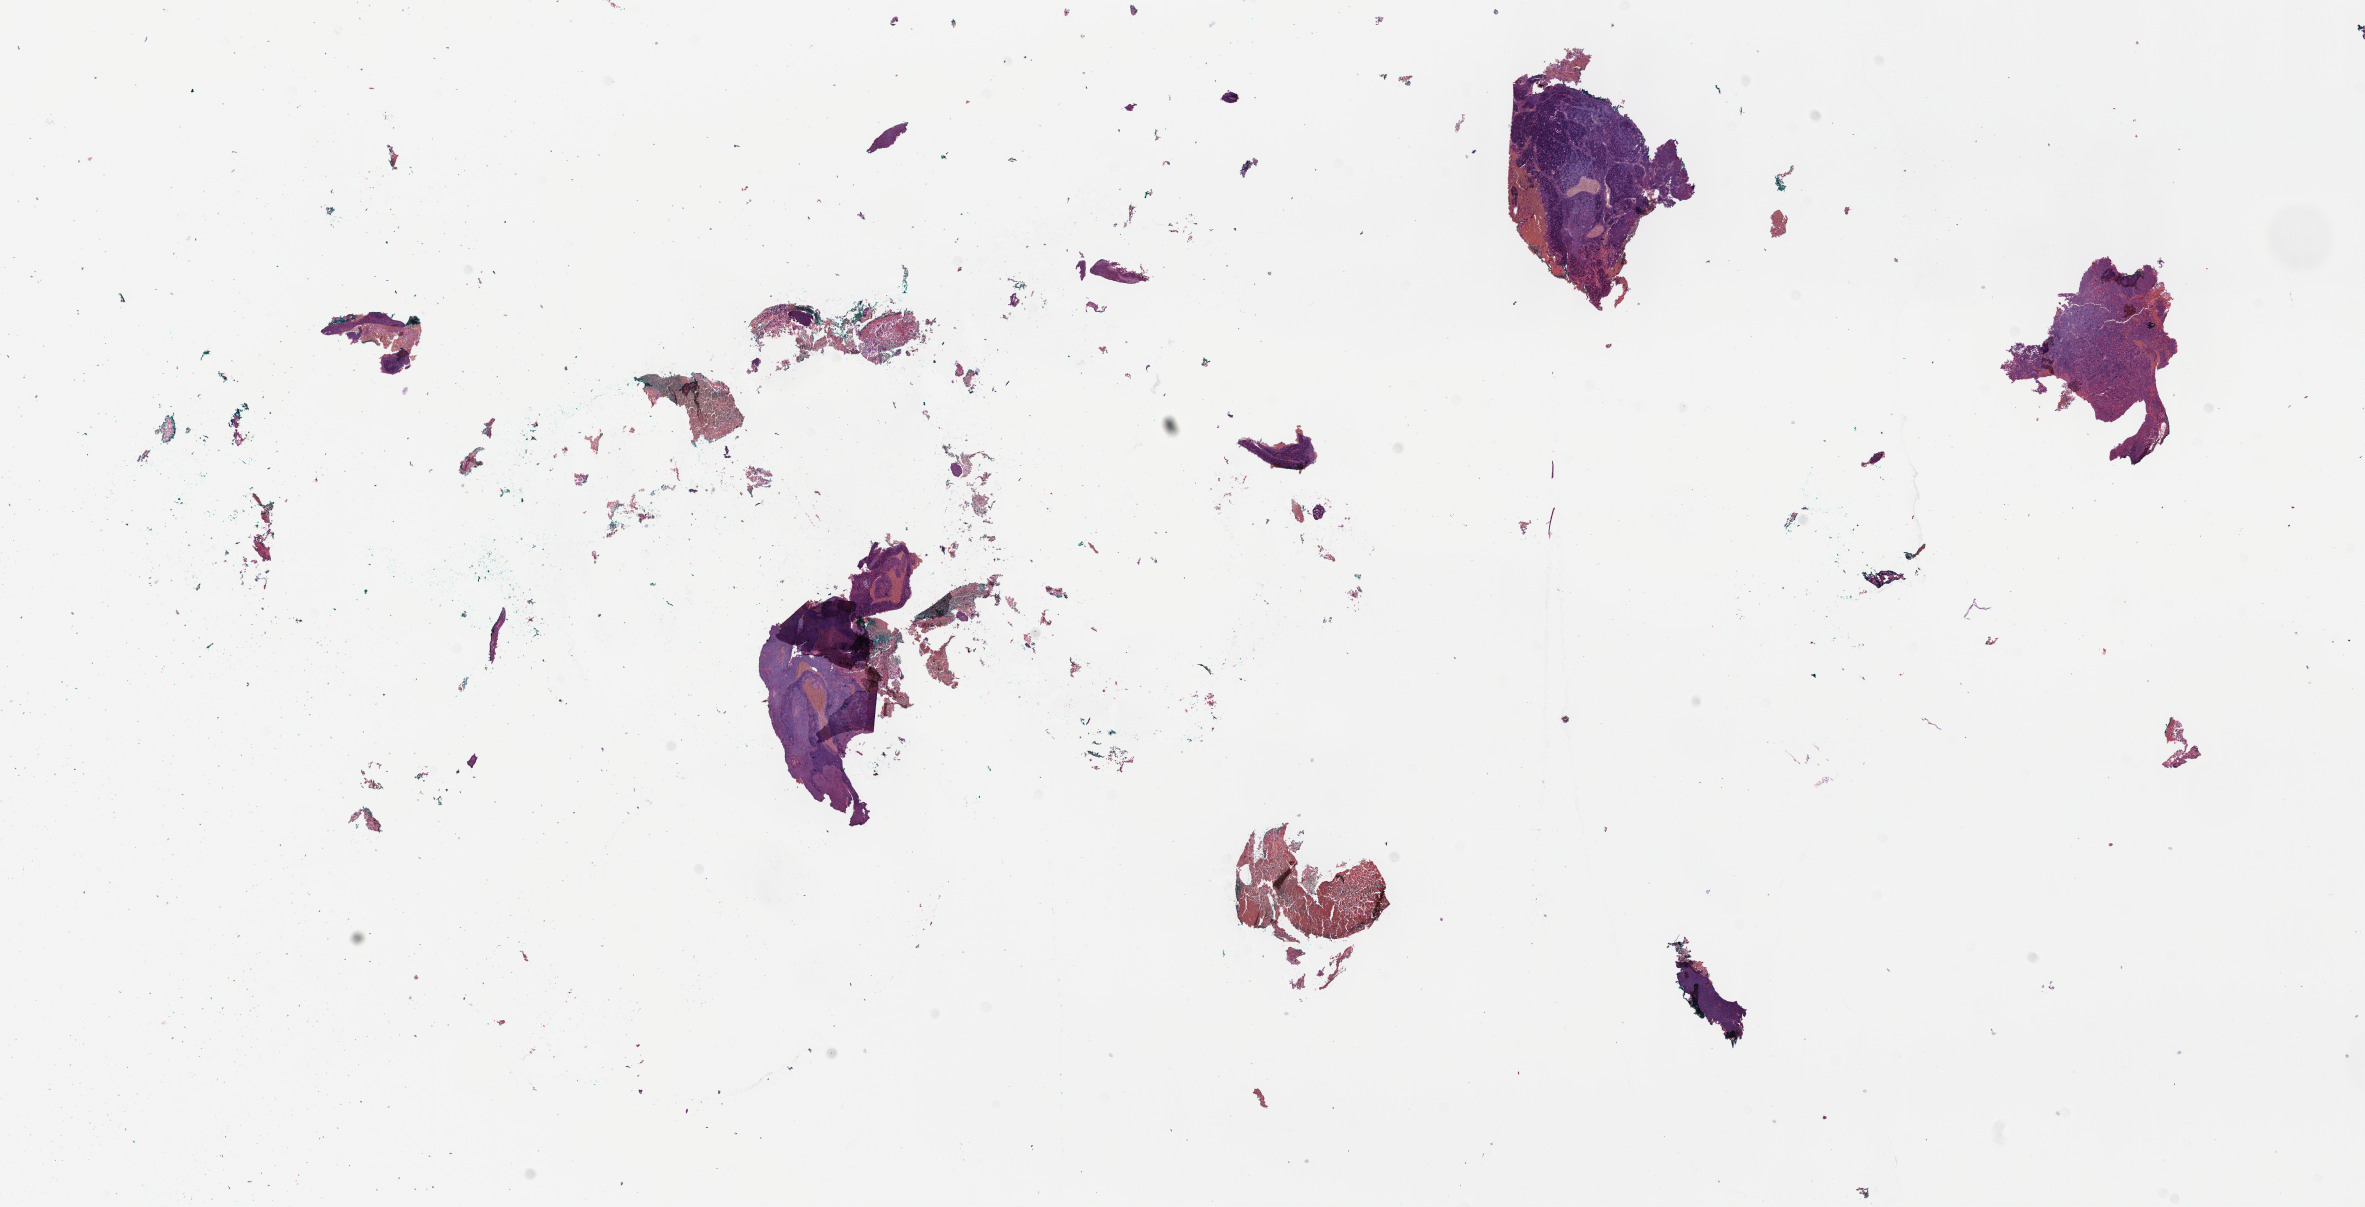
Whole-slide histology image, Hematoxylin and eosin (H&E) stained, shown as a low-resolution overview of the whole scanned area (about 19.1 x 9.8 mm), formalin-fixed paraffin-embedded (FFPE) diagnostic section, cervix, primary tumour sample. Patient: female, age at initial diagnosis 62 years. Histologic grade: G3 (poorly differentiated).
* FIGO stage: IVB
* diagnosis: Squamous cell carcinoma, NOS (cervix uteri)